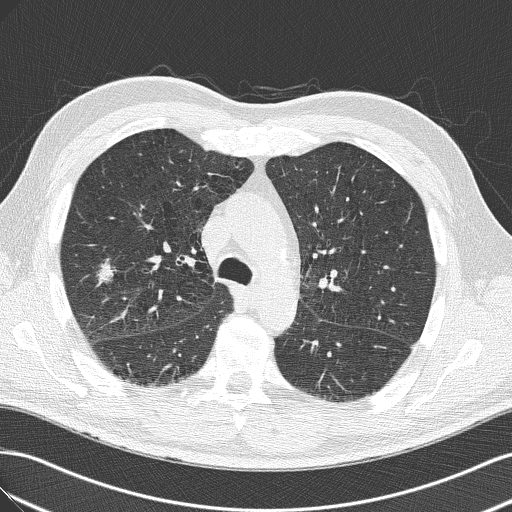
Low-dose screening chest CT, one axial slice. Position 90 of 143 along the scan axis. Reconstruction kernel B50f. 120 kVp. Lung window (W 1500 / L -600 HU). 2 mm slice thickness. 512 × 512 image matrix.
Structures marked on this image (manually delineated by an expert):
- lesion 1 (tumor, lower lobe of right lung): bounding box <97,261,115,286> (left, top, right, bottom; pixels)